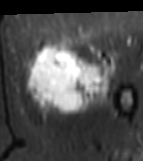
MRI of an extremity soft-tissue mass, one axial slice; position 26 of 81 along the scan axis; STIR; MR volume resampled by the dataset authors to the PET/CT grid (not the native acquisition matrix); 3.27 mm slice thickness; 143 × 161 image matrix. Female patient. Case-level facts recorded for this patient, not image findings: histological type: myxofibrosarcoma; grade: intermediate; site of the primary tumour: left thigh.
Structures marked on this image (expert contour drawn on MRI and transferred to this co-registered scan by the dataset authors):
- gross tumour volume including surrounding oedema: bounding box [x1, y1, x2, y2] px = [24, 42, 116, 114]
- gross tumour volume (mass): [26, 47, 112, 112]